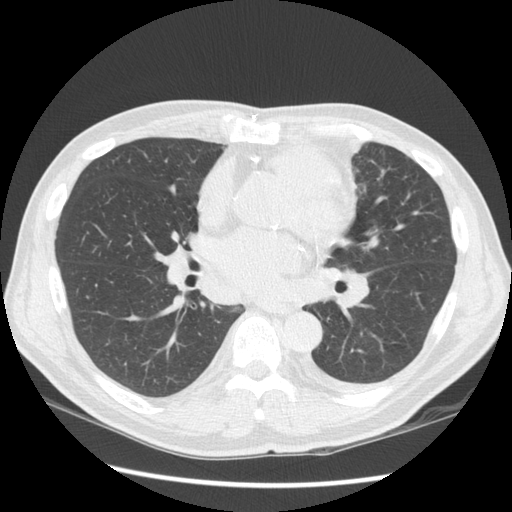
Low-dose screening chest CT, one axial slice; position 71 of 136 along the scan axis; reconstruction kernel STANDARD; 120 kVp; lung window (W 1500 / L -600 HU); 512 × 512 image matrix, field of view 360 × 360 mm.
Annotated regions visible in this slice (outlined manually by an expert reader):
- lesion 1 (tumor, upper lobe of left lung): bounding box (x1, y1, x2, y2) in pixels: (334, 138, 363, 164)